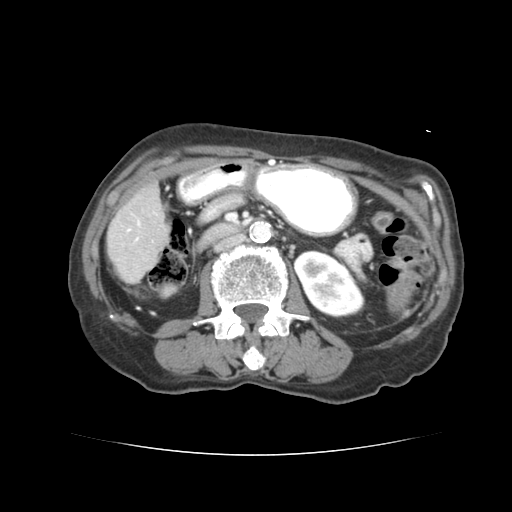
Contrast-enhanced abdominal CT (liver protocol), one axial slice; reconstruction kernel STANDARD; soft-tissue window (W 400 / L 40 HU); 512 × 512 image matrix, field of view 340 × 340 mm. From the clinical record (not read from this slice): diagnosis: hepatocellular carcinoma (patient treated with transarterial chemoembolisation; whether this scan precedes or follows treatment is not stated here); TNM stage (as recorded): Stage-I; Child-Pugh class: A; tumour differentiation: well differentiated; tumour nodularity: uninodular.
Outlined on this slice (semi-automatically segmented with operator editing):
- liver parenchyma outside the tumour (the mass and vessels are separate outlines, so this box may not span the whole liver): box from (x=108, y=160) to (x=174, y=276) px
- liver vessels: (x=119, y=213)–(x=153, y=241)